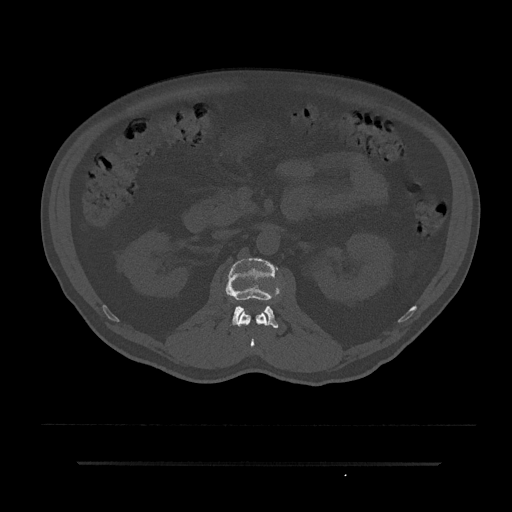
CT including the spine, one axial slice; slice 106 of 797 in the series (ordered by position); 120 kVp; bone window (W 1800 / L 400 HU); 512 × 512 image matrix, field of view 464 × 464 mm. Male patient, age 59 years. Case-level facts recorded for this patient, not image findings: primary cancer: bile ducts.
Structures marked on this image (semi-automatically segmented with operator editing):
- L1 vertebra: bounding box <238,311,268,348> (left, top, right, bottom; pixels)
- L2 vertebra: <226,258,279,328>